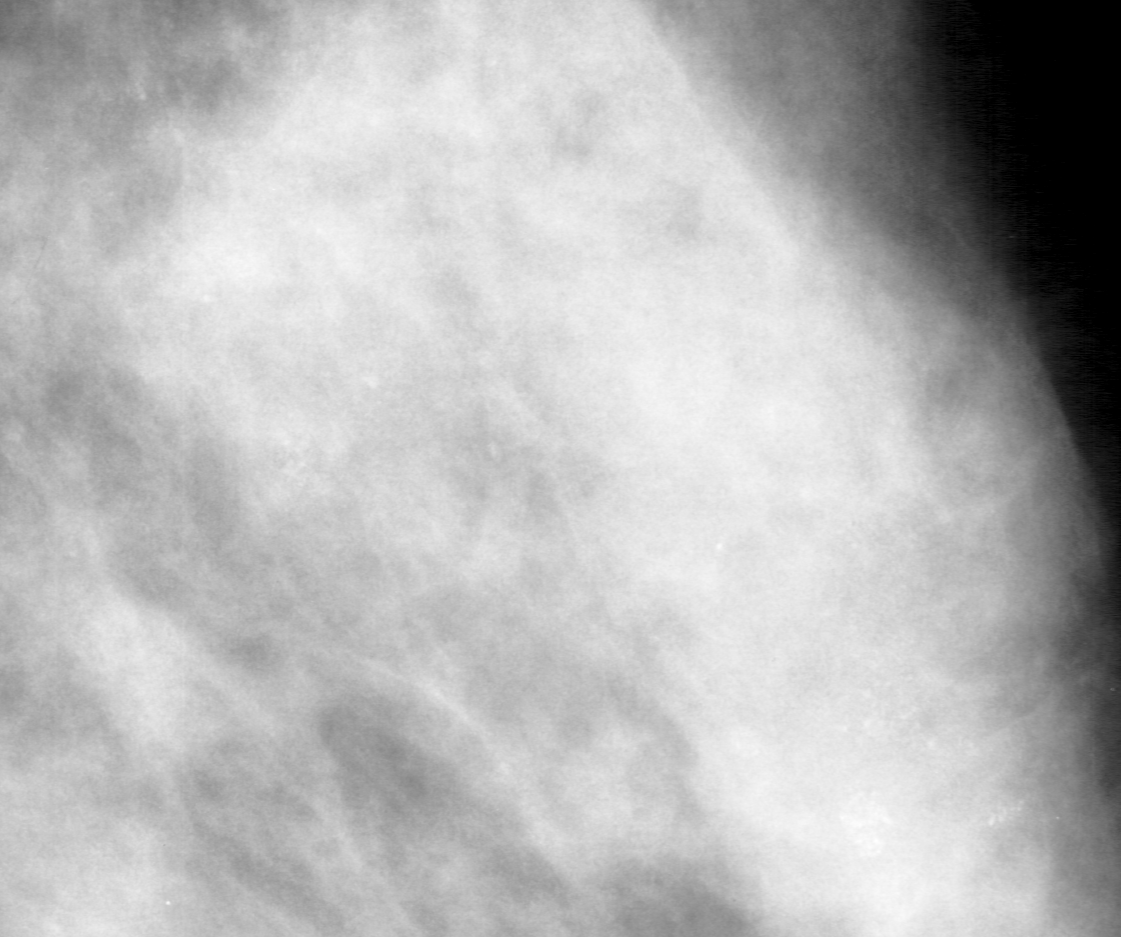
Crop from a digitized film mammogram around one marked abnormality; right breast; MLO view.
Finding: calcifications, morphology pleomorphic, distribution segmental; BI-RADS assessment category 4; pathology (as recorded): malignant.